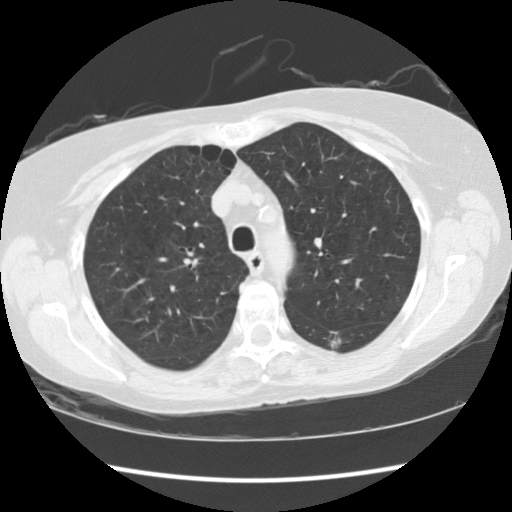
Low-dose screening chest CT, one axial slice. 120 kVp. Lung window (W 1500 / L -600 HU). 2.5 mm slice thickness. 512 × 512 image matrix, field of view 334 × 334 mm.
Structures marked on this image (outlined manually by an expert reader):
- lesion 1 (tumor, lower lobe of left lung): bounding box (x1, y1, x2, y2) in pixels: (330, 331, 341, 348)